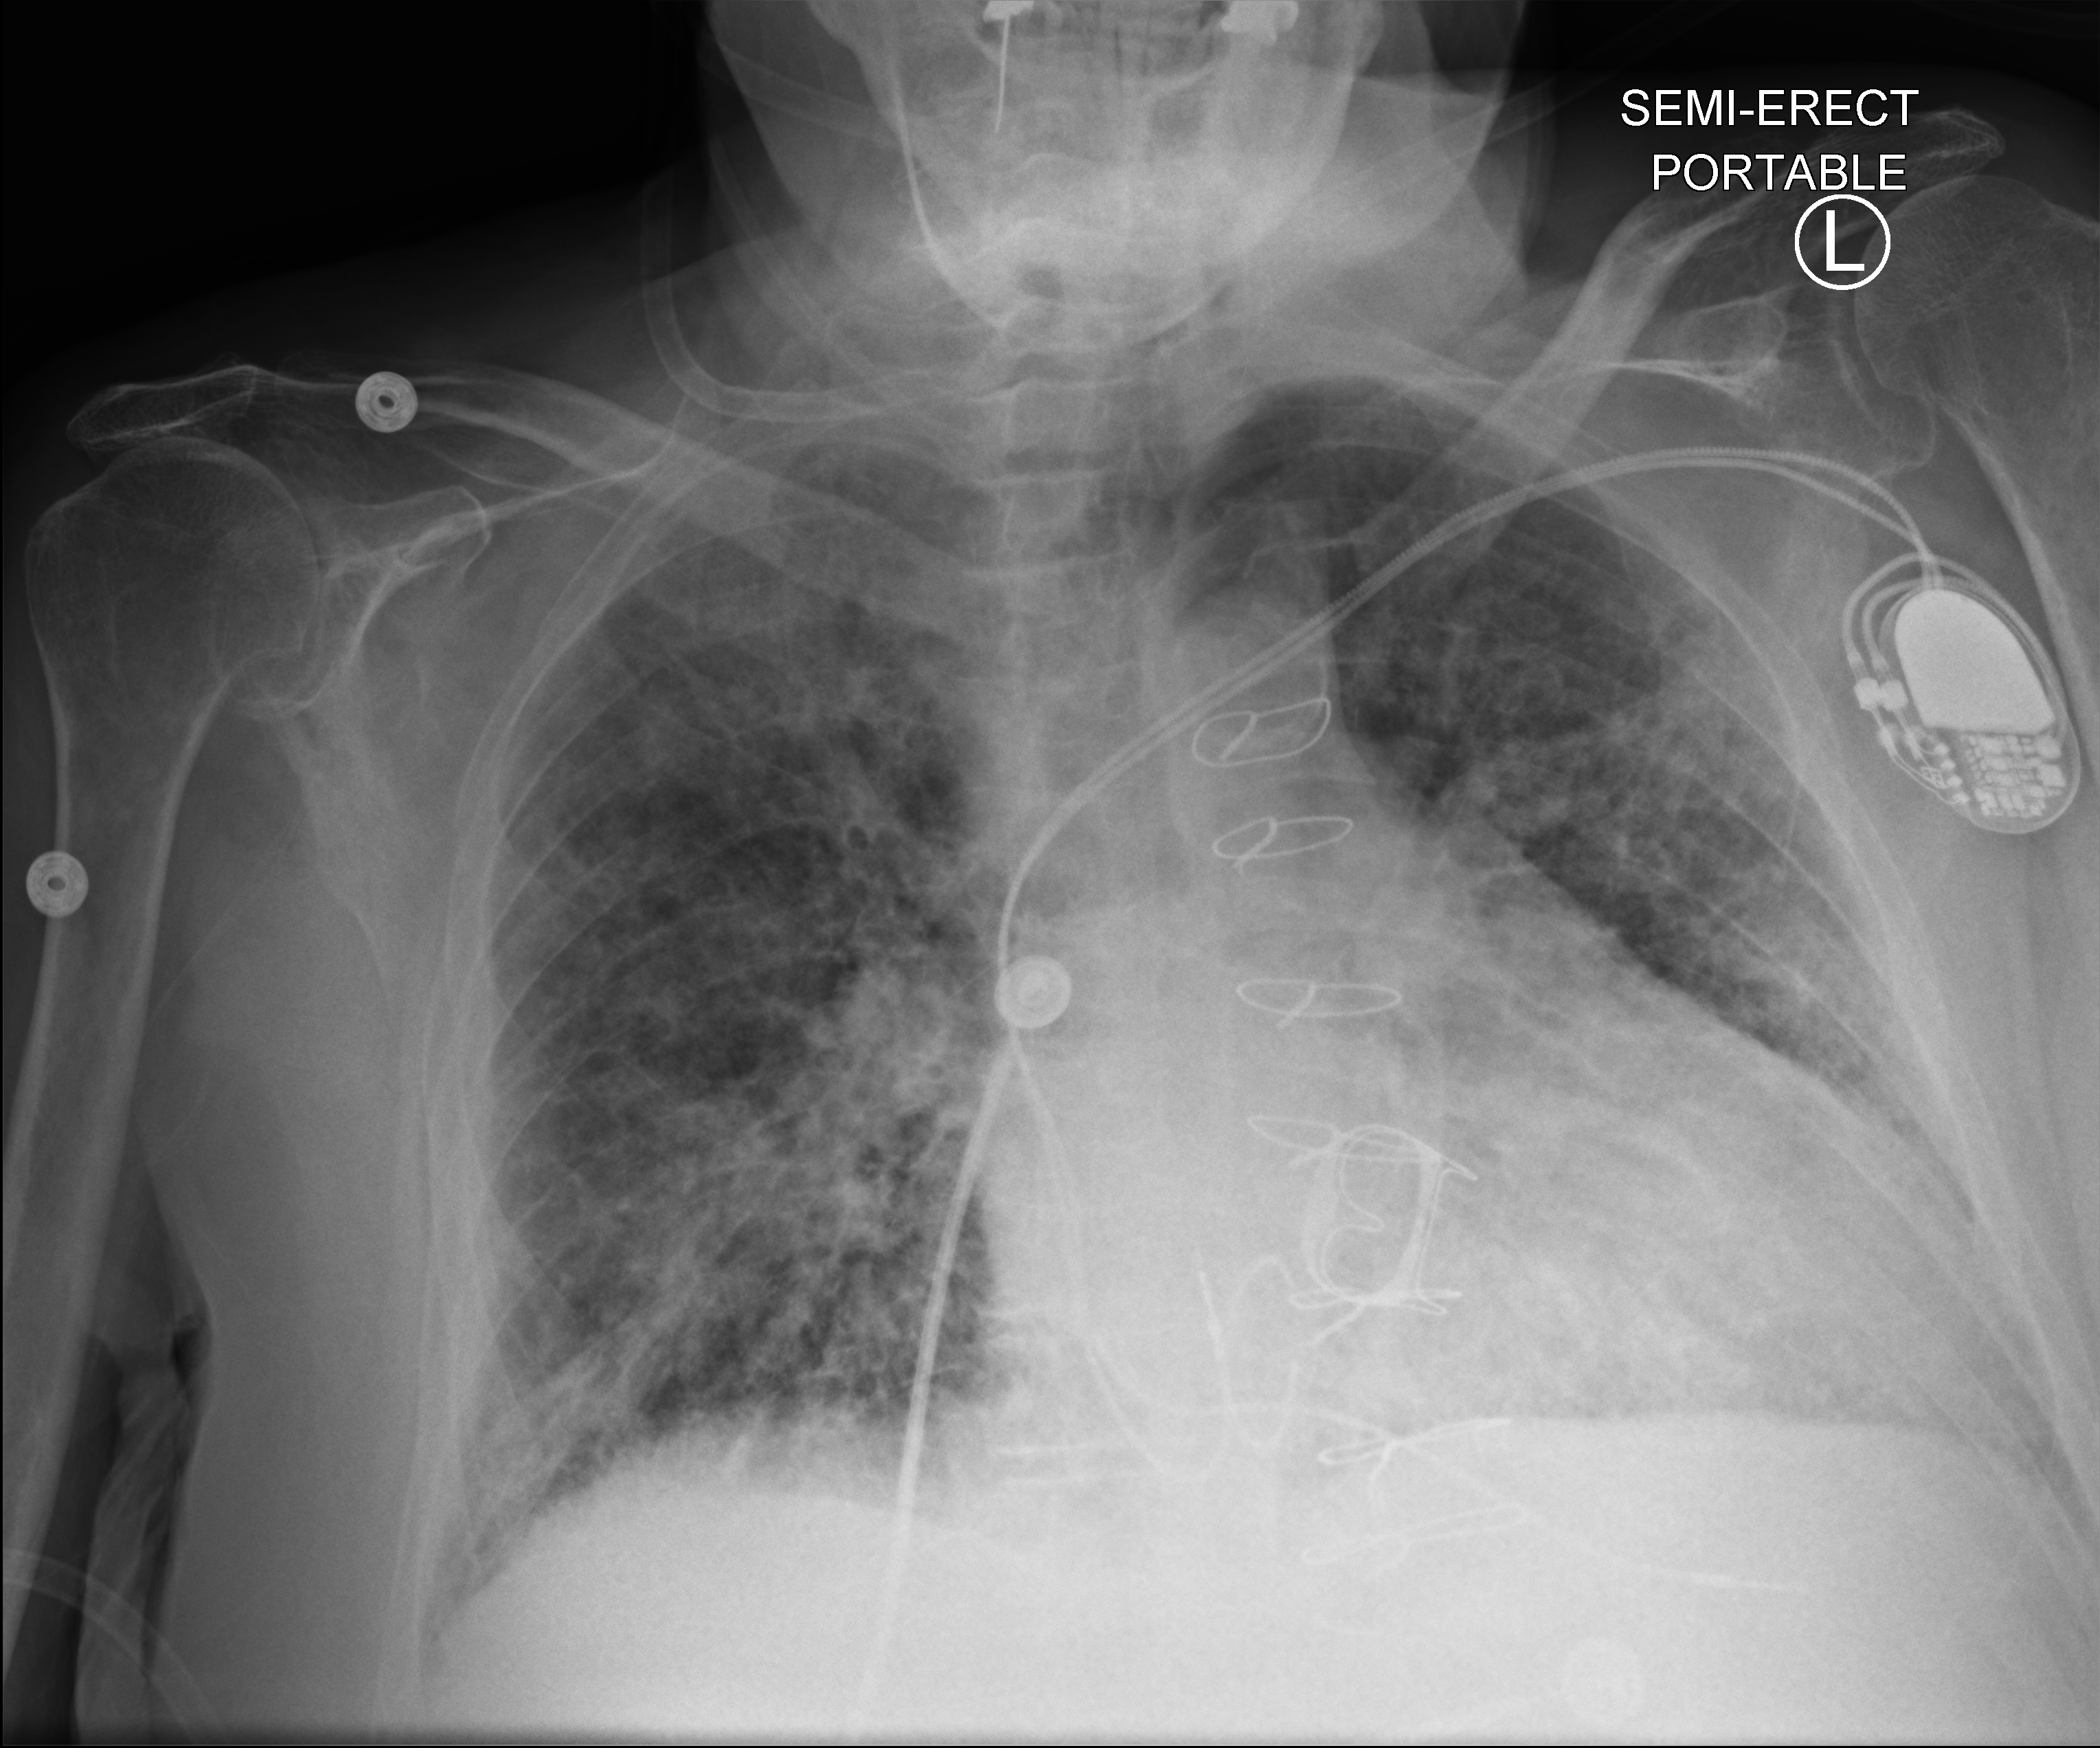
Chest X-ray (portable), anteroposterior (AP) projection. Male patient hospitalised with COVID-19, age 75–90 years.
Admission-level facts for this patient (not findings on this image; timing relative to this image not recorded): hypertension (admission record): yes; length of hospital stay: 13 days; admitted to intensive care during this hospital stay: no.